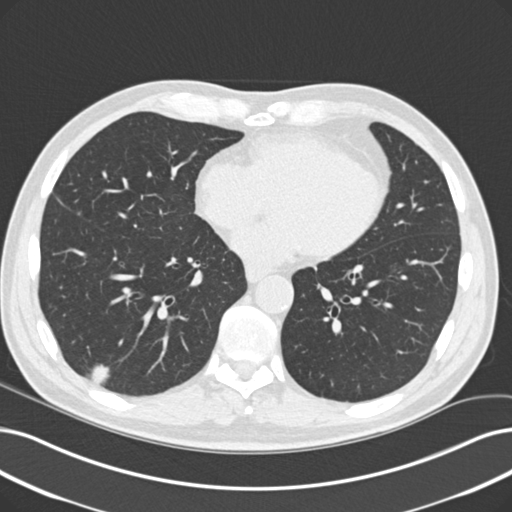
Chest CT (low-dose screening protocol), one axial image; baseline annual screen; lung window (W 1500 / L -600 HU); 2 mm slice thickness. Male participant, aged 60 years at enrolment. Former smoker at enrolment.
Expert reader's lesion annotation, bounding box <75,357,117,402> (left, top, right, bottom; pixels). The screening reader recorded 2 non-calcified nodules or masses ≥4 mm on this exam (right lower lobe, left lower lobe); which of them this box marks is not recorded. Participant outcome: lung cancer diagnosed 64 days after this screen — acinar cell carcinoma, right lower lobe, moderately differentiated (G2), stage IA (AJCC 6th edition), 16 mm at pathology.